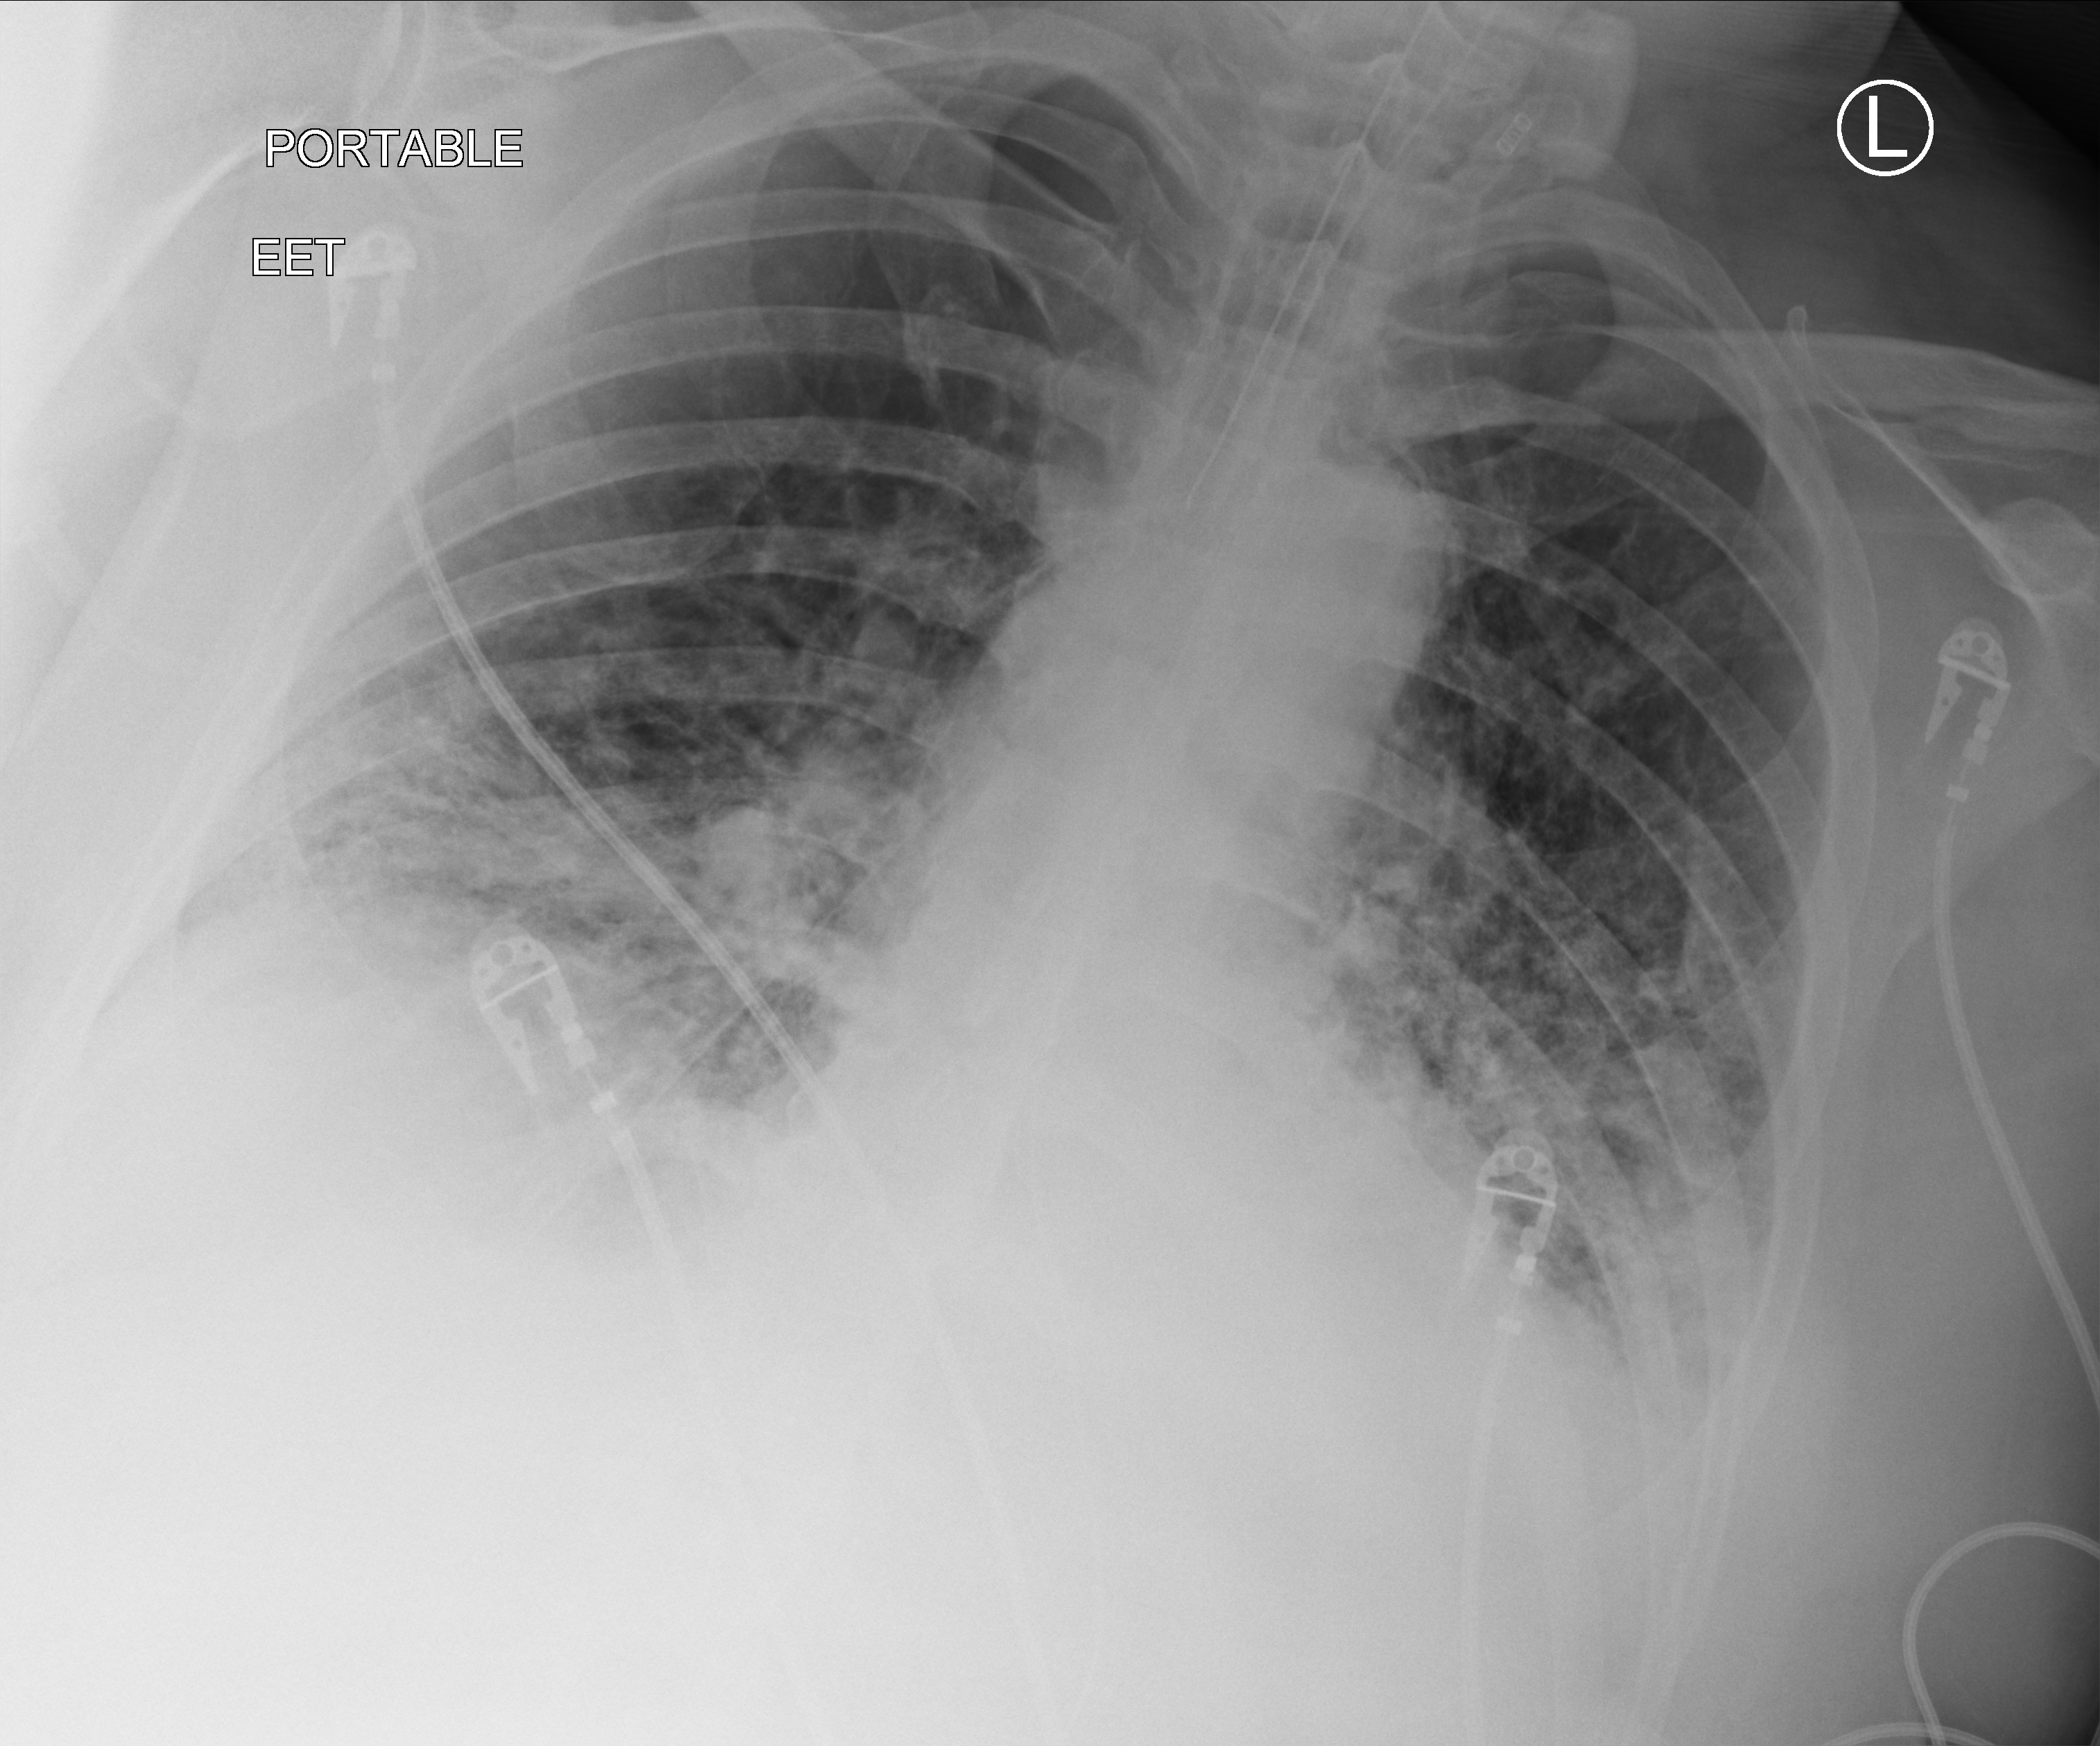
Portable chest radiograph, anteroposterior (AP) projection. Adult patient hospitalised with COVID-19, age 18–59 years.
Admission-level facts for this patient (not findings on this image; timing relative to this image not recorded):
- admitted to intensive care during this hospital stay: yes
- mechanically ventilated during this hospital stay: yes